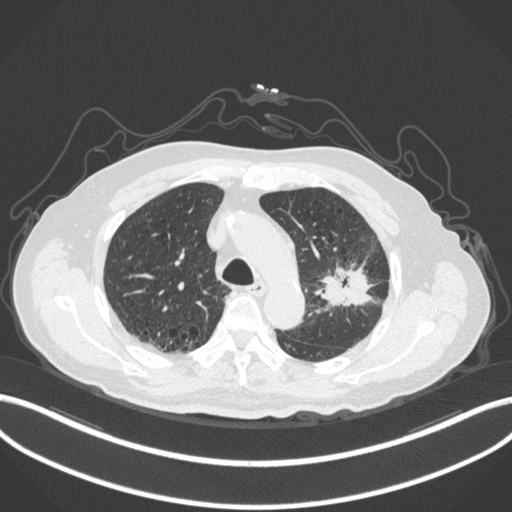
Chest CT, one axial slice; position 215 of 331 along the scan axis; 120 kVp; lung window (W 1500 / L -600 HU); 1 mm slice thickness; 512 × 512 image matrix. Patient: male, 79 years. From the clinical record (not read from this slice): clinical TNM (as recorded): T2a N1 M1.
Outlined on this slice (rectangle marked by the reading radiologist):
- lung tumour (recorded histology: adenocarcinoma): box from (x=323, y=266) to (x=374, y=309) px